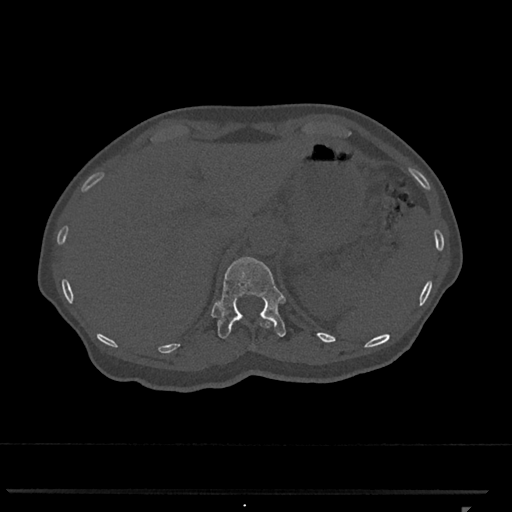
CT including the spine, one axial slice. Slice 476 of 793 in the series (ordered by position). Reconstruction kernel Br40s/3. Bone window (W 1800 / L 400 HU). 0.5 mm slice thickness. 512 × 512 image matrix. Female patient, age 62 years. Case-level facts recorded for this patient, not image findings: primary cancer: renal.
Annotated regions visible in this slice (semi-automatic segmentation, software-assisted and operator-edited):
- T11 vertebra: bounding box (x1, y1, x2, y2) in pixels: (261, 322, 271, 328)
- T12 vertebra: (216, 257, 286, 338)